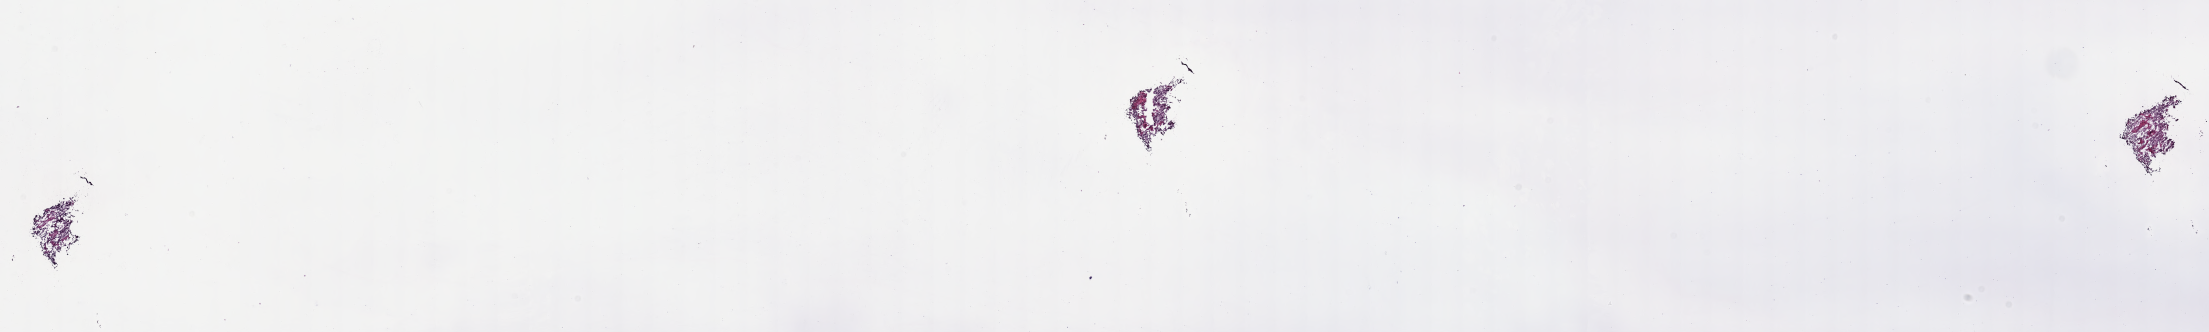
Whole-slide image, hematoxylin and eosin (H&E) stain of tumor tissue from the cerebellum — shown as a low-resolution overview of the whole scanned area (about 35.7 x 5.4 mm). Cryosection (OCT / tissue freezing medium). Male patient, age 200 months (16 years 8 months).
• recorded diagnosis: Medulloblastoma, NOS